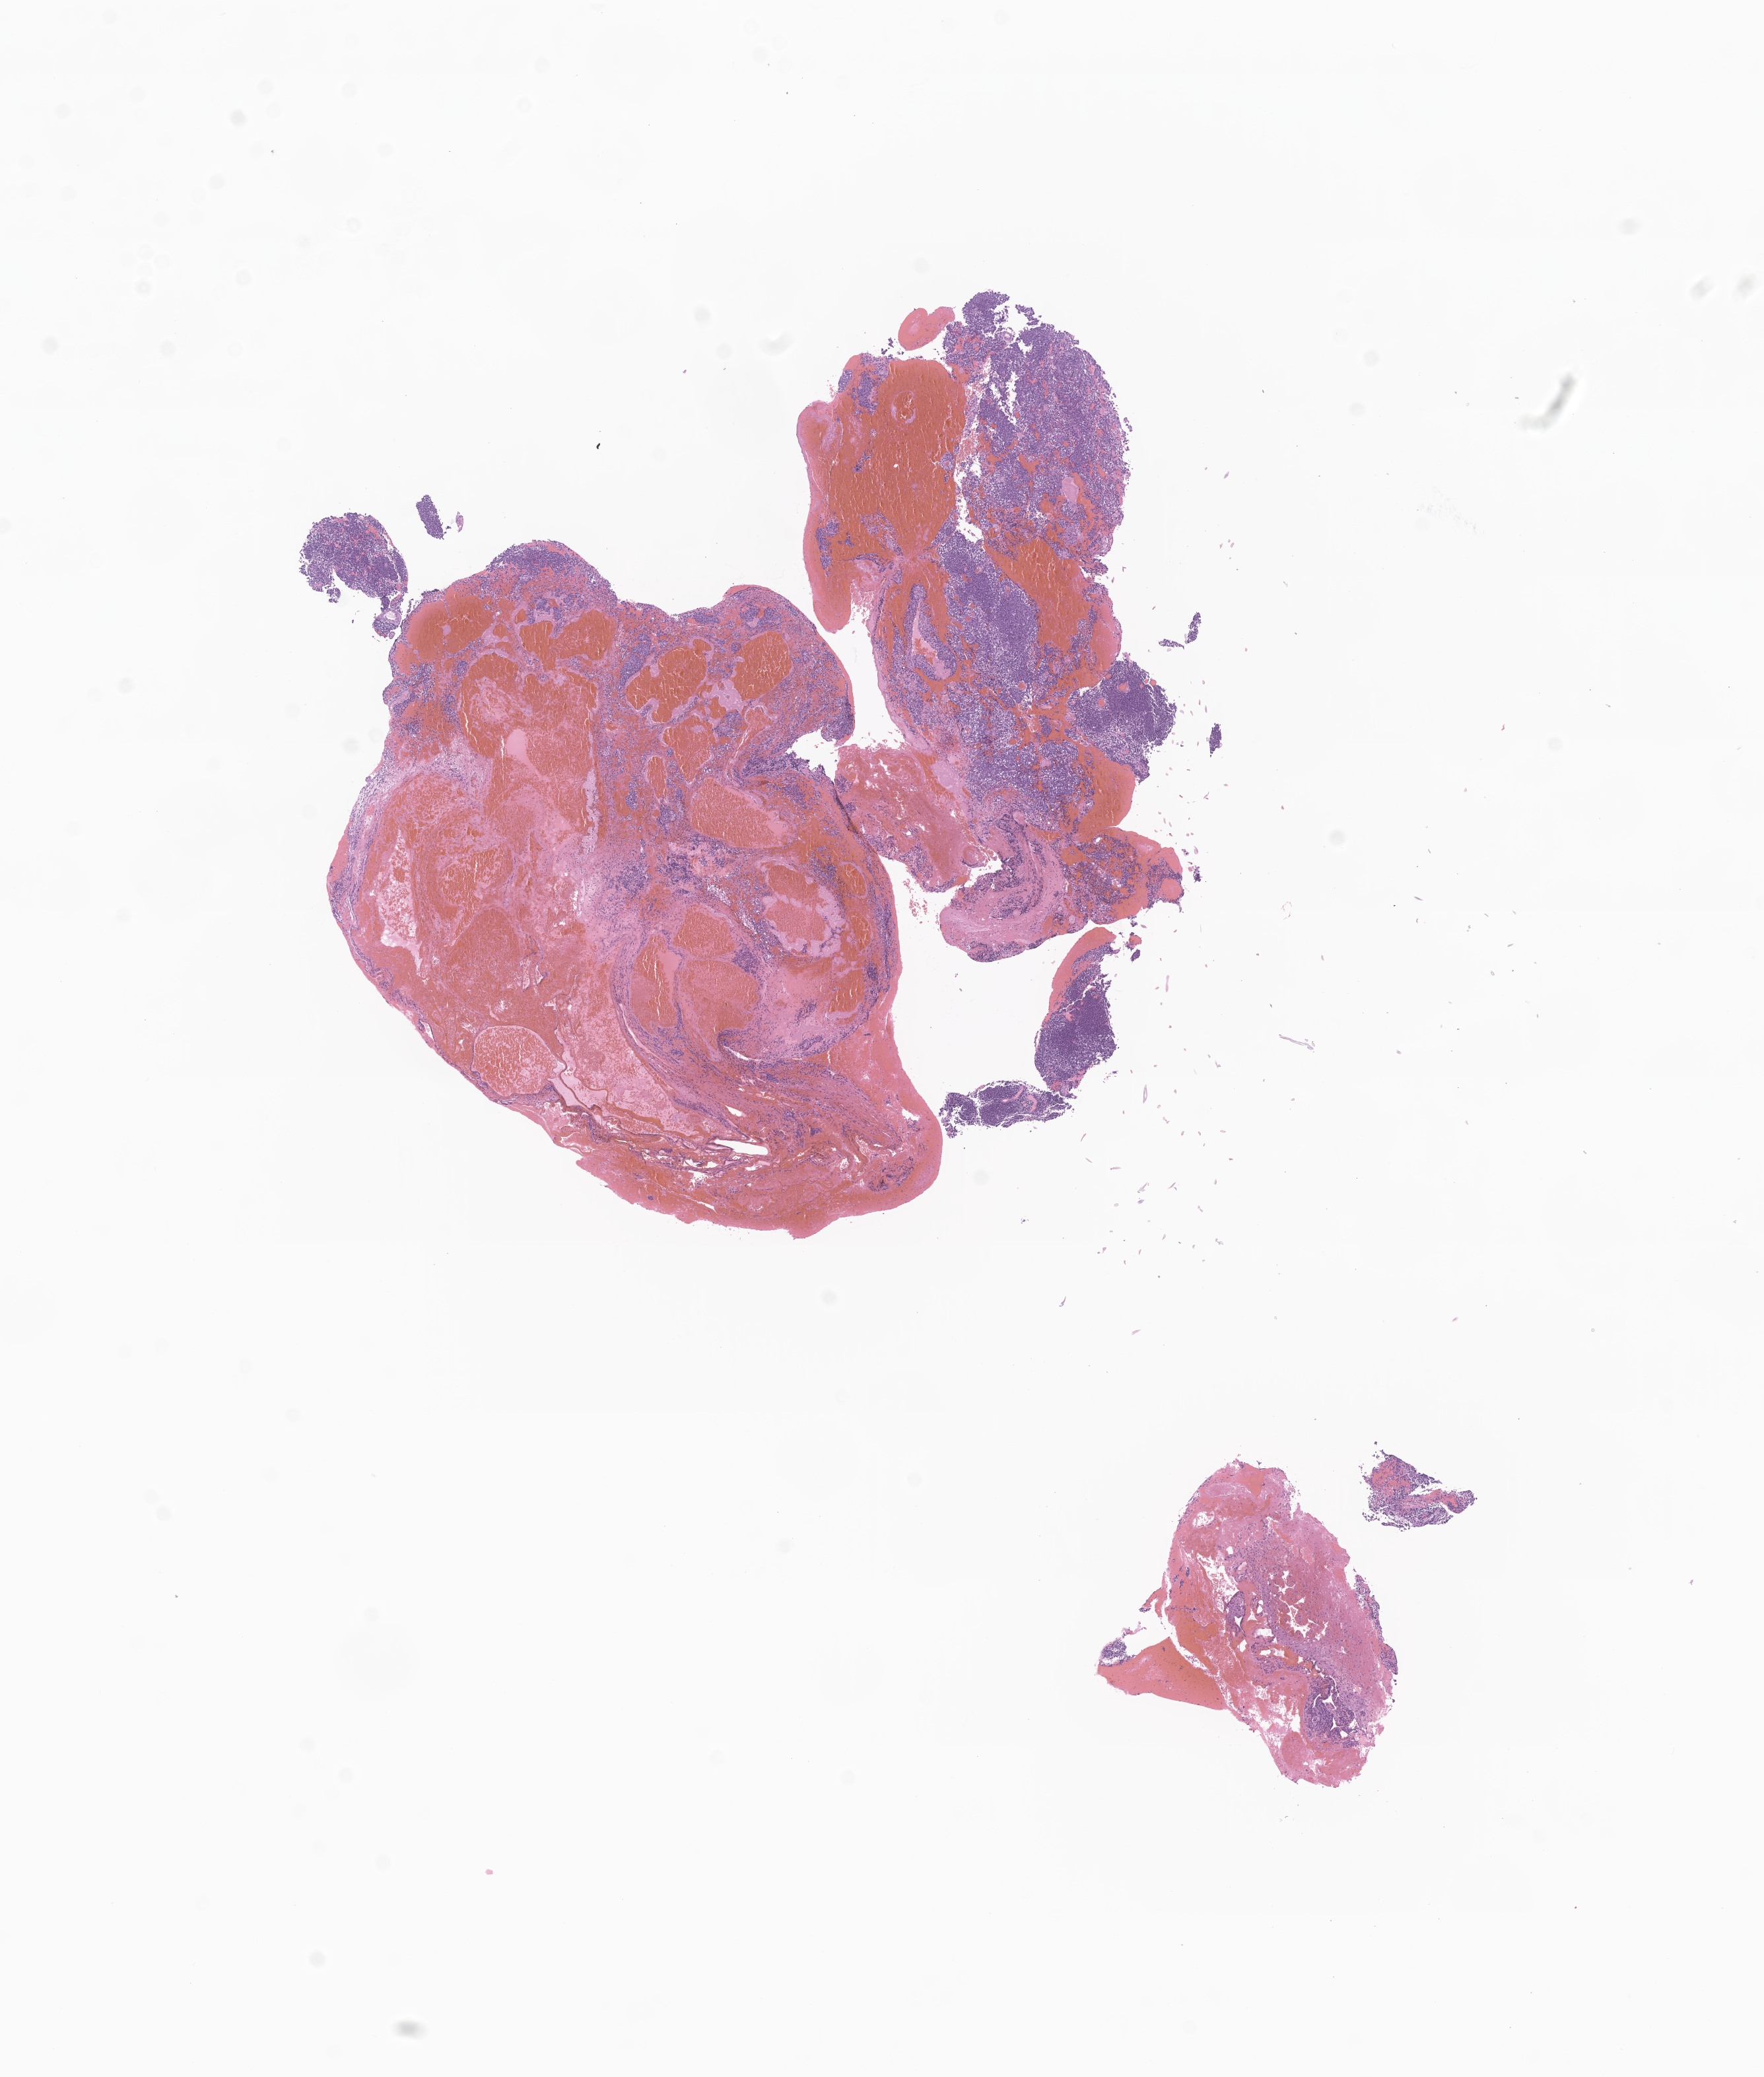
Hematoxylin and eosin (H&E) whole-slide image of tumor tissue from the brain — a low-resolution overview of the entire scanned area, about 11.3 x 13.3 mm. Formalin-fixed, paraffin-embedded (FFPE) tissue. Female patient, age 152 months (12 years 8 months).
Diagnosis: Medulloblastoma, NOS.